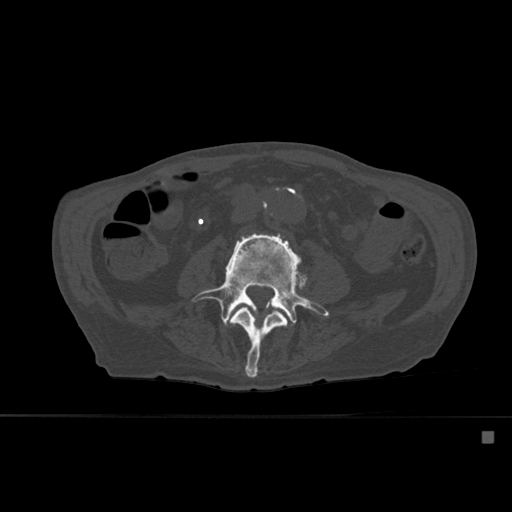
CT including the spine, one axial slice. Bone window (W 1800 / L 400 HU). 1.5 mm slice thickness. 512 × 512 image matrix, field of view 373 × 373 mm. Patient: male, 78 years. Case-level facts recorded for this patient, not image findings: primary cancer: prostate.
Structures marked on this image (semi-automatically segmented with operator editing):
- L3 vertebra: bounding box <228,307,288,378> (left, top, right, bottom; pixels)
- L4 vertebra: <191,233,330,326>